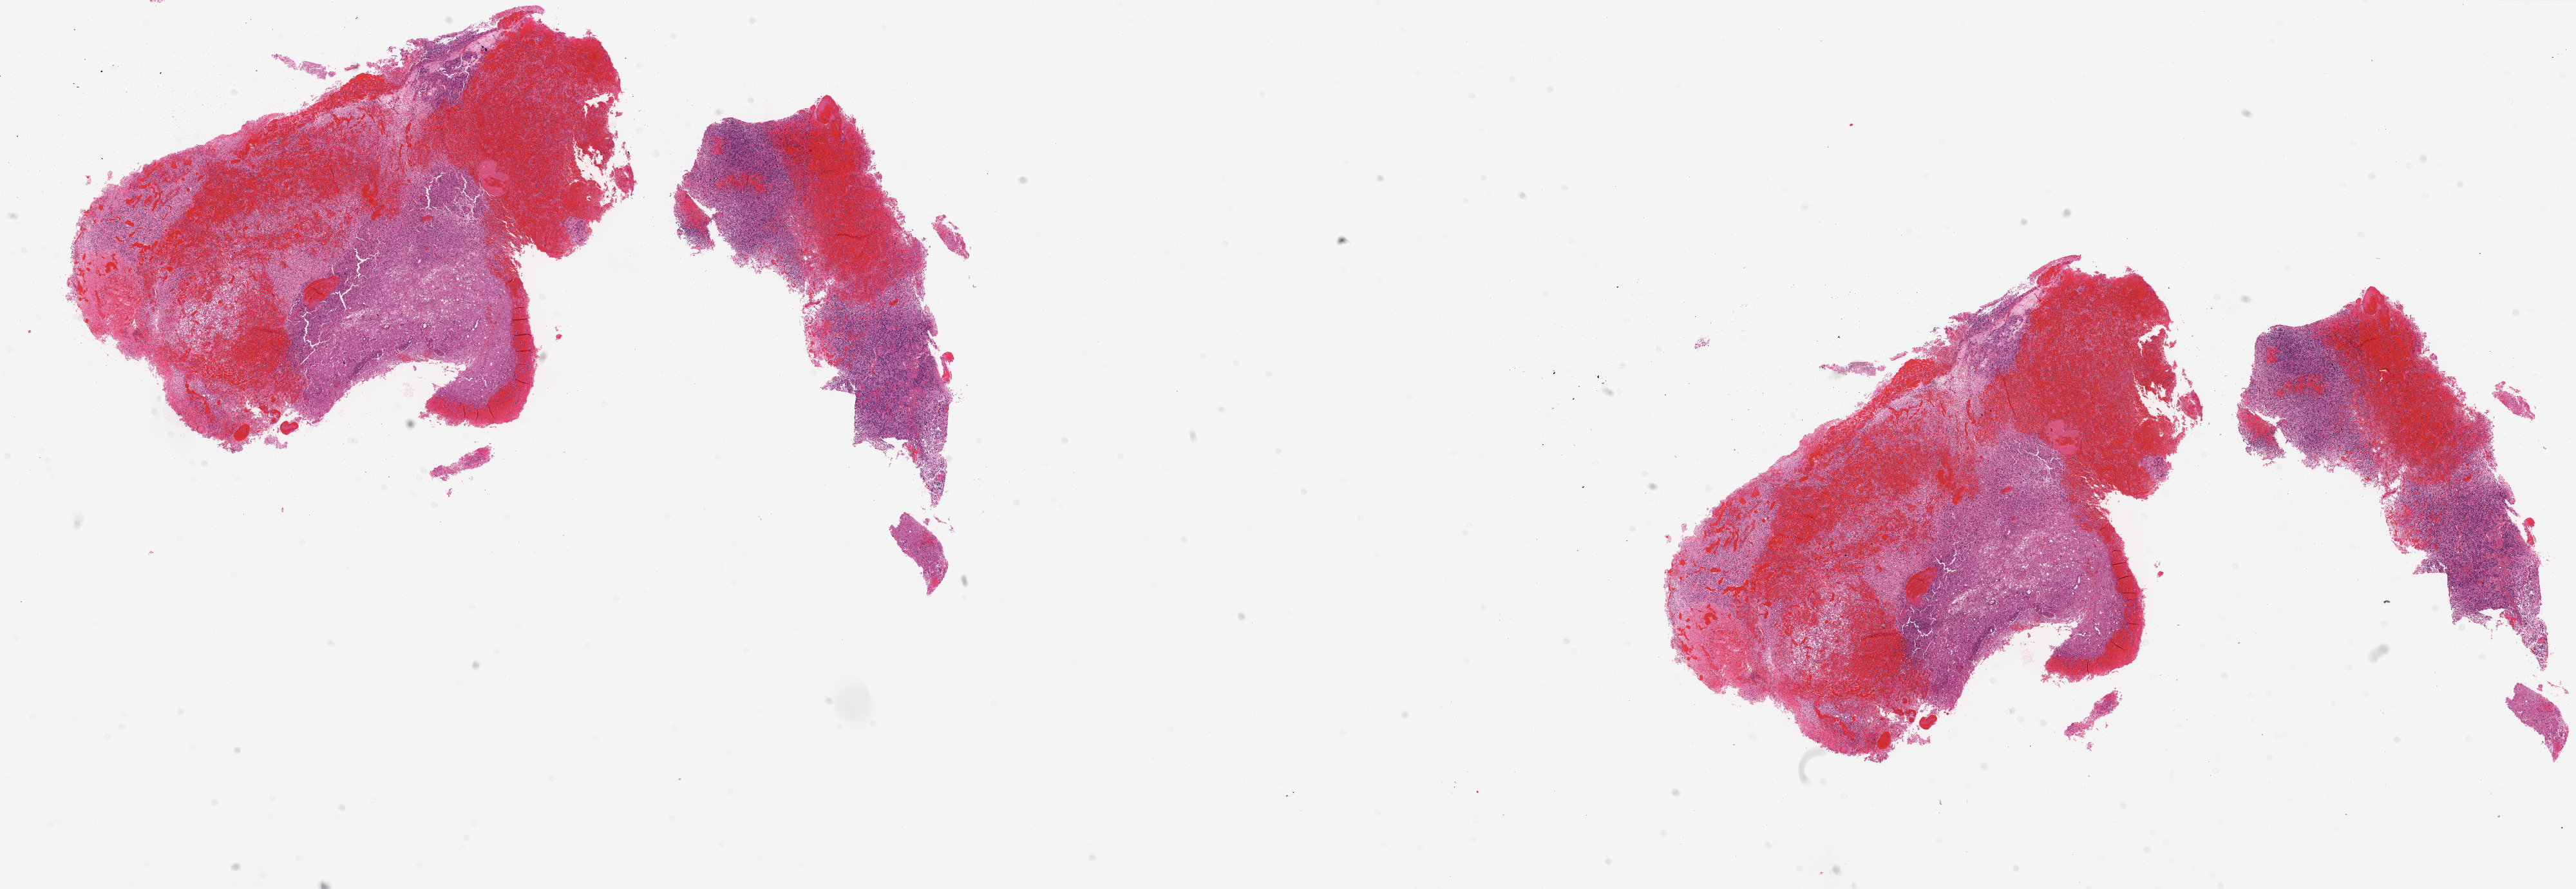
H&E whole-slide image, shown as a low-resolution overview of the whole scanned area (about 32.1 x 11.1 mm, from a 20x scan). Frozen section from the top of the tissue portion. Primary tumour sample from the brain. Patient: male, age at initial diagnosis 53 years. Composition of this section per pathologist review: tumour cells 100%, tumour nuclei 80%, normal cells 0%, stromal cells 0%, necrosis 0%.
Histologic diagnosis: Glioblastoma.